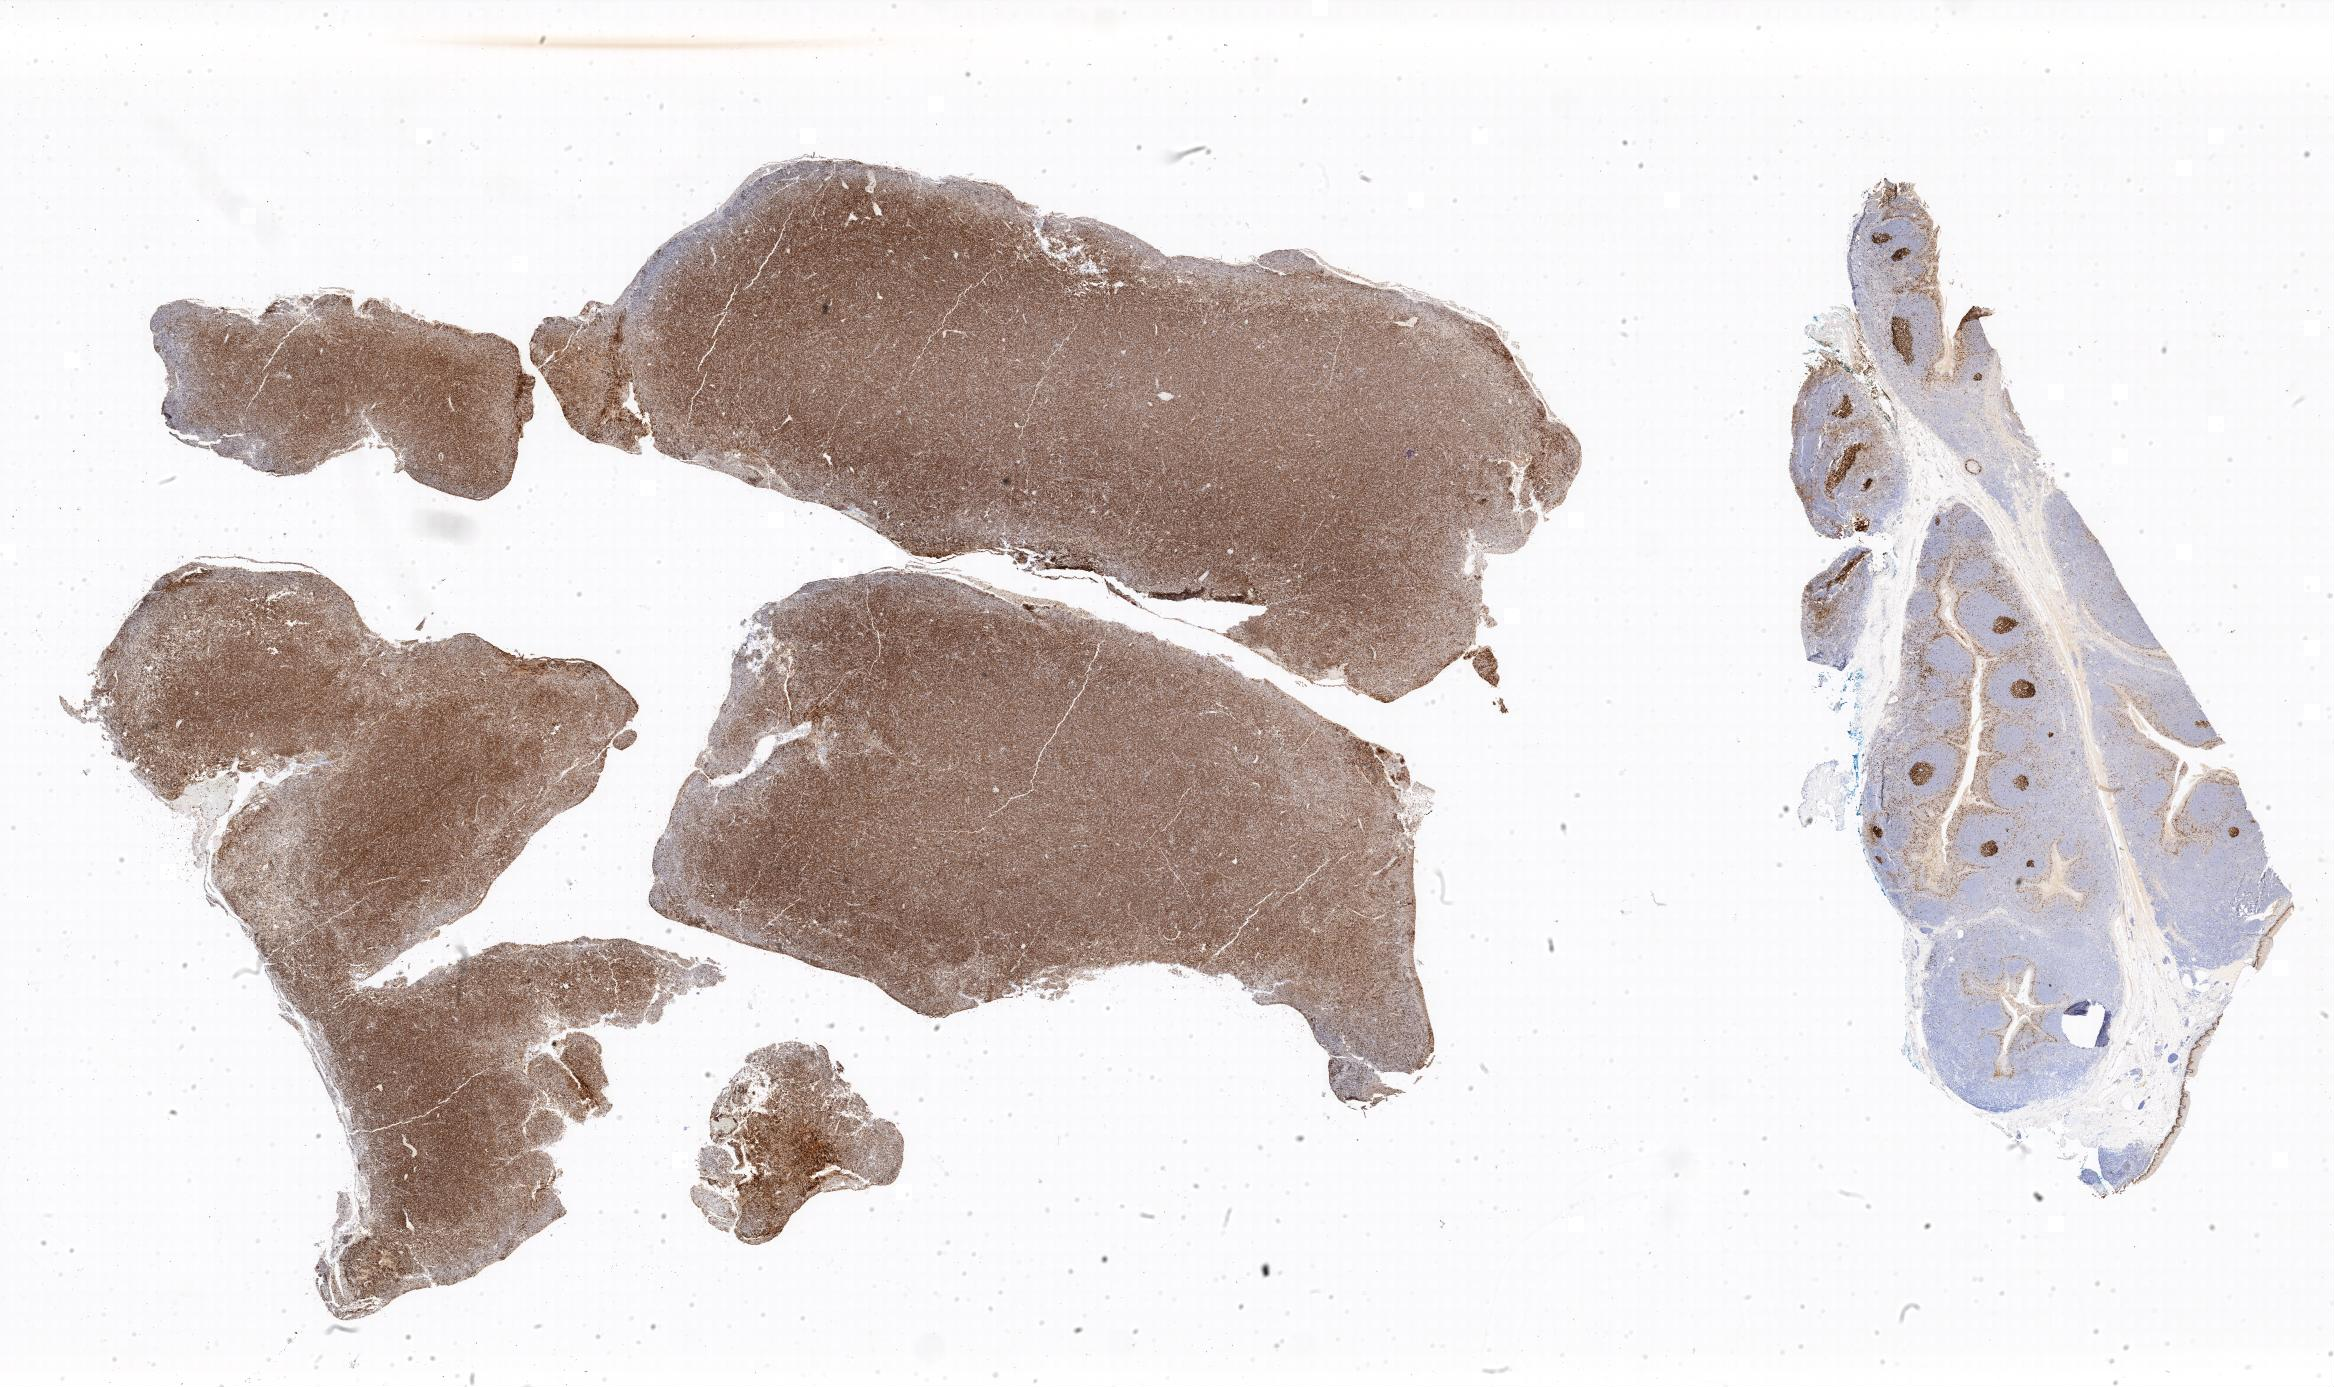
Whole-slide image, immunohistochemical stain for Ki-67, low-resolution overview of the scanned area; specimen: tumor tissue; anatomic site: peritoneum. Female, age 7 years at initial diagnosis.
* histologic diagnosis: Burkitt lymphoma, NOS